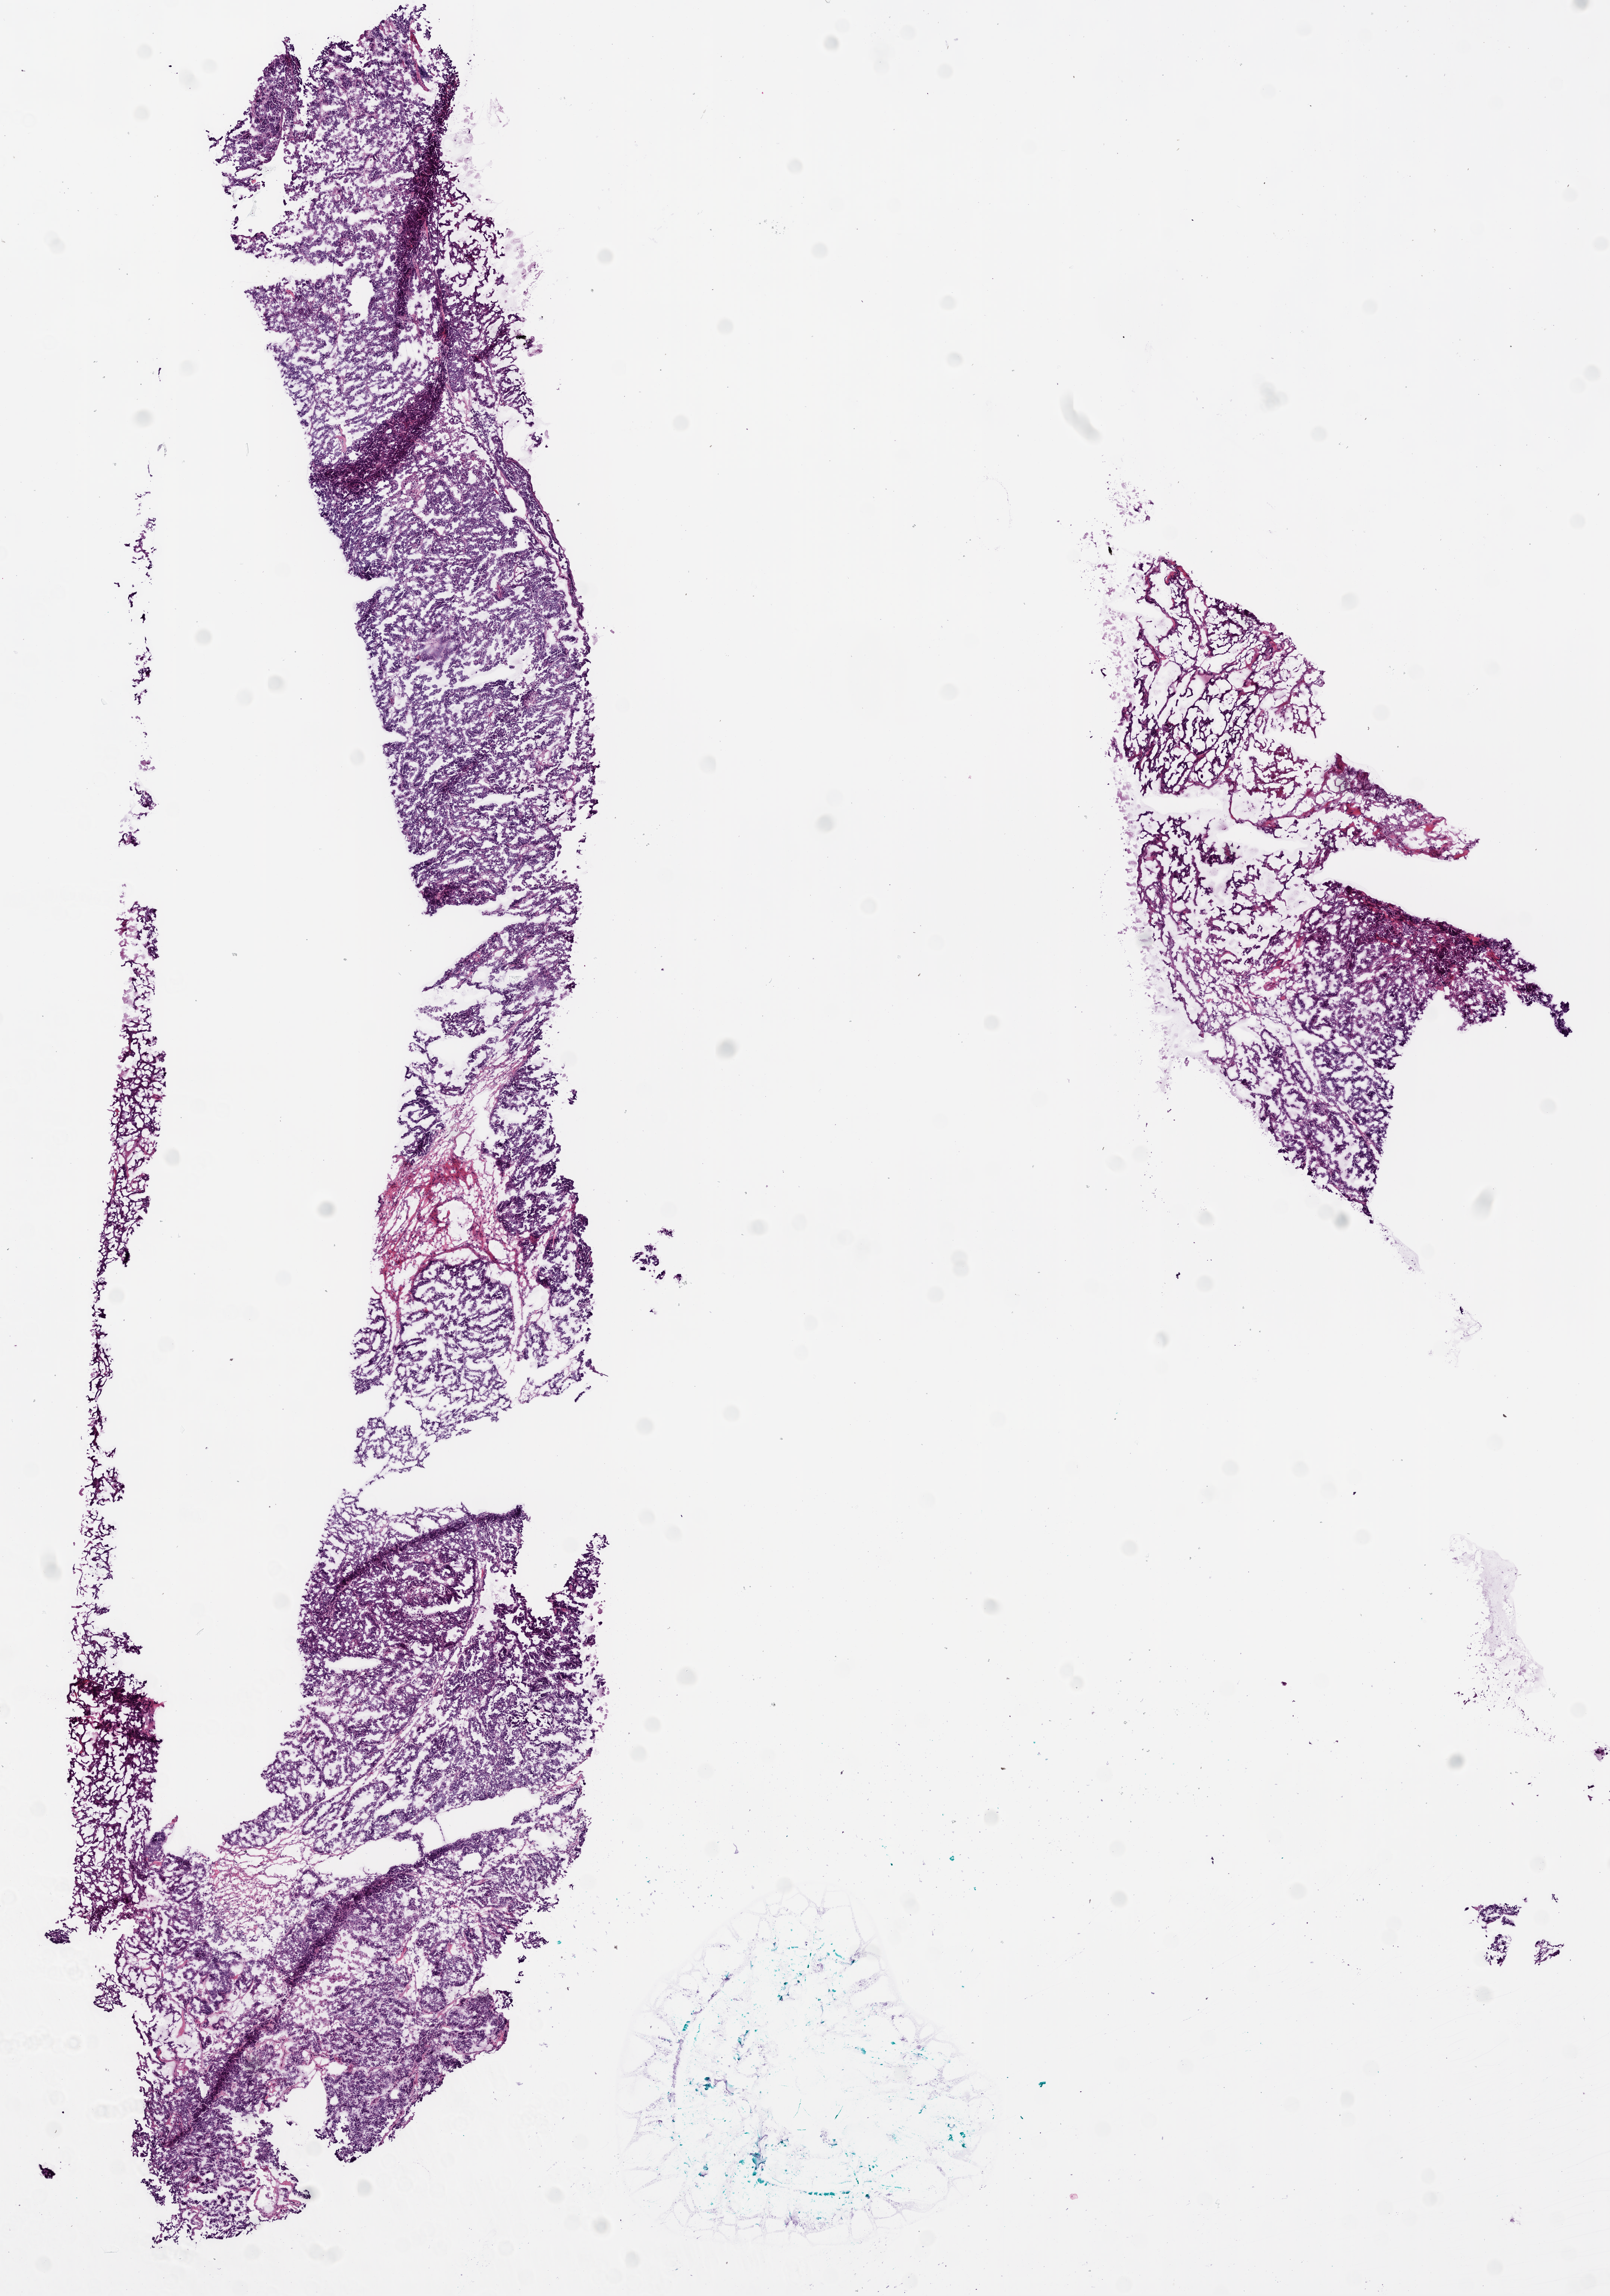
Digitized Hematoxylin and eosin (H&E) stained tissue section (whole slide) — low-resolution overview of the scanned area, about 8.7 x 12.4 mm (from a 20x scan); frozen section from the bottom of the tissue portion; primary tumour sample from the ovary. Female, age 53 years at initial diagnosis. Histologic grade: G2 (moderately differentiated). Pathologist review of this section (percent, as recorded): tumour cells 90%, tumour nuclei 99%, stromal cells 5%, necrosis 5%.
FIGO stage: IIIC. Histologic diagnosis: Serous cystadenocarcinoma, NOS.